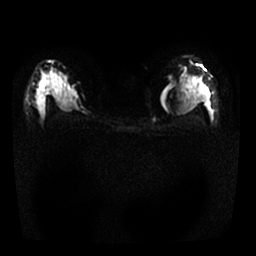
Breast MRI, one axial slice; position 14 of 25 along the scan axis; diffusion-weighted series; image 2 of 4 stored at this slice position (different b-values; order by instance number); 1.5 T; 4 mm slice thickness; 256 × 256 image matrix. Female patient.
Annotated regions visible in this slice (manually delineated by an expert):
- tumour on diffusion-weighted imaging: bounding box <40,82,45,91> (left, top, right, bottom; pixels)